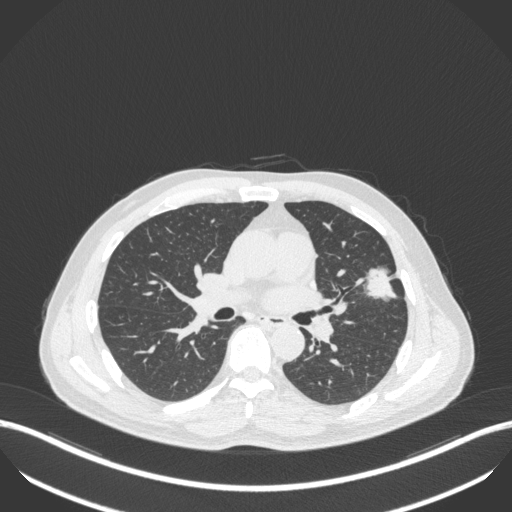
Chest CT, one axial slice. Reconstruction kernel B31f. Lung window (W 1500 / L -600 HU). 1 mm slice thickness. 512 × 512 image matrix, field of view 400 × 400 mm. Male patient, age 55 years. Case-level facts recorded for this patient, not image findings: clinical TNM (as recorded): T1c N0 M0; histopathological grade: G2-3.
Structures marked on this image (bounding box drawn by a radiologist):
- lung tumour (recorded histology: adenocarcinoma): bounding box (x1, y1, x2, y2) in pixels: (362, 262, 401, 305)